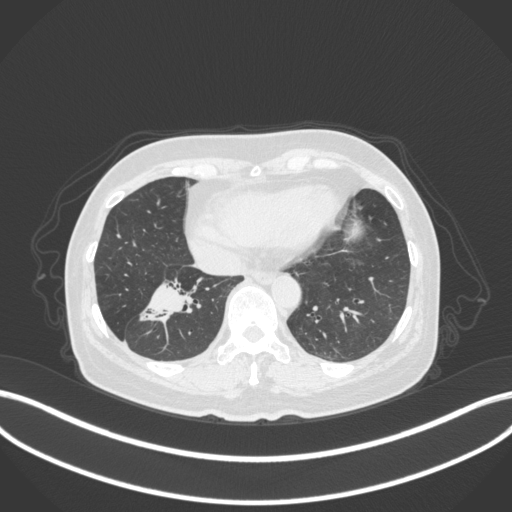
Chest CT, one axial slice; reconstruction kernel B31f; 120 kVp; lung window (W 1500 / L -600 HU); 512 × 512 image matrix. Female patient, age 67 years. Case-level facts recorded for this patient, not image findings: clinical TNM (as recorded): T1c N1 M0.
Annotated regions visible in this slice (rectangle marked by the reading radiologist):
- lung tumour (recorded histology: adenocarcinoma): bounding box <137,275,205,328> (left, top, right, bottom; pixels)